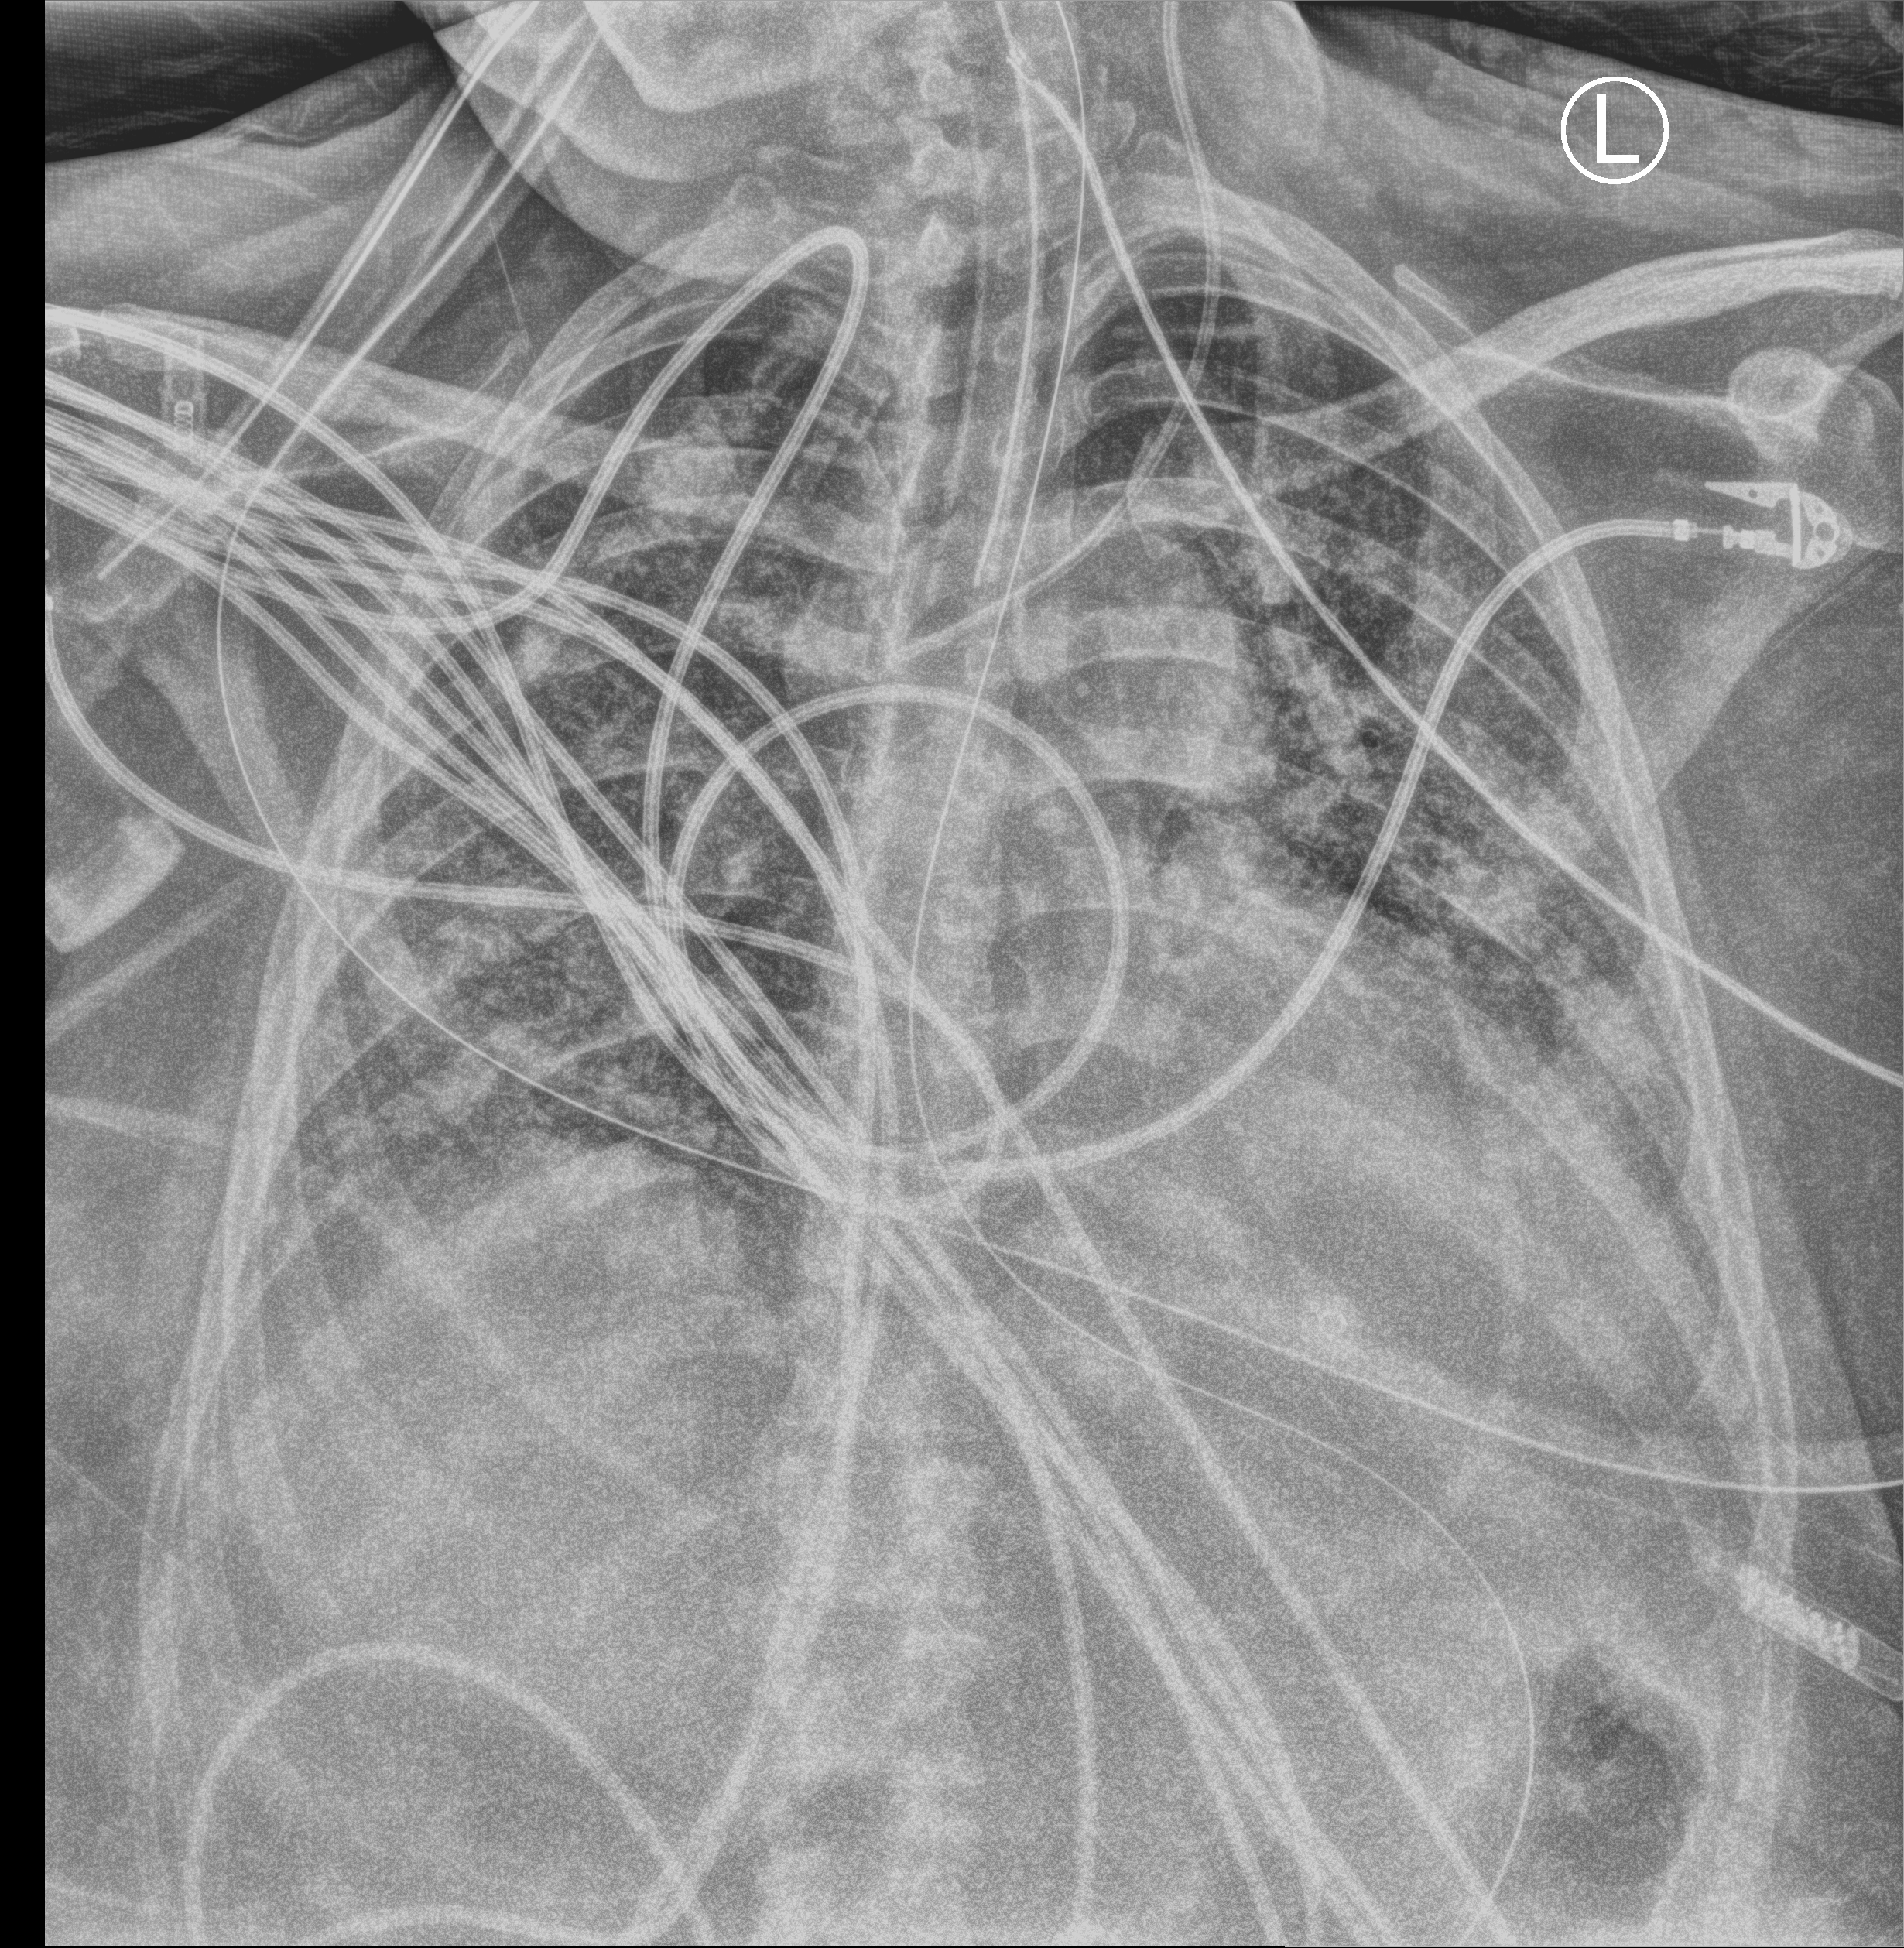
Chest X-ray (portable). Patient hospitalised with COVID-19; female, aged 18–59 years.
From the hospital-stay record, not from the radiograph (when in the stay this image was taken is not recorded):
- length of hospital stay: 33 days
- admitted to intensive care during this hospital stay: no